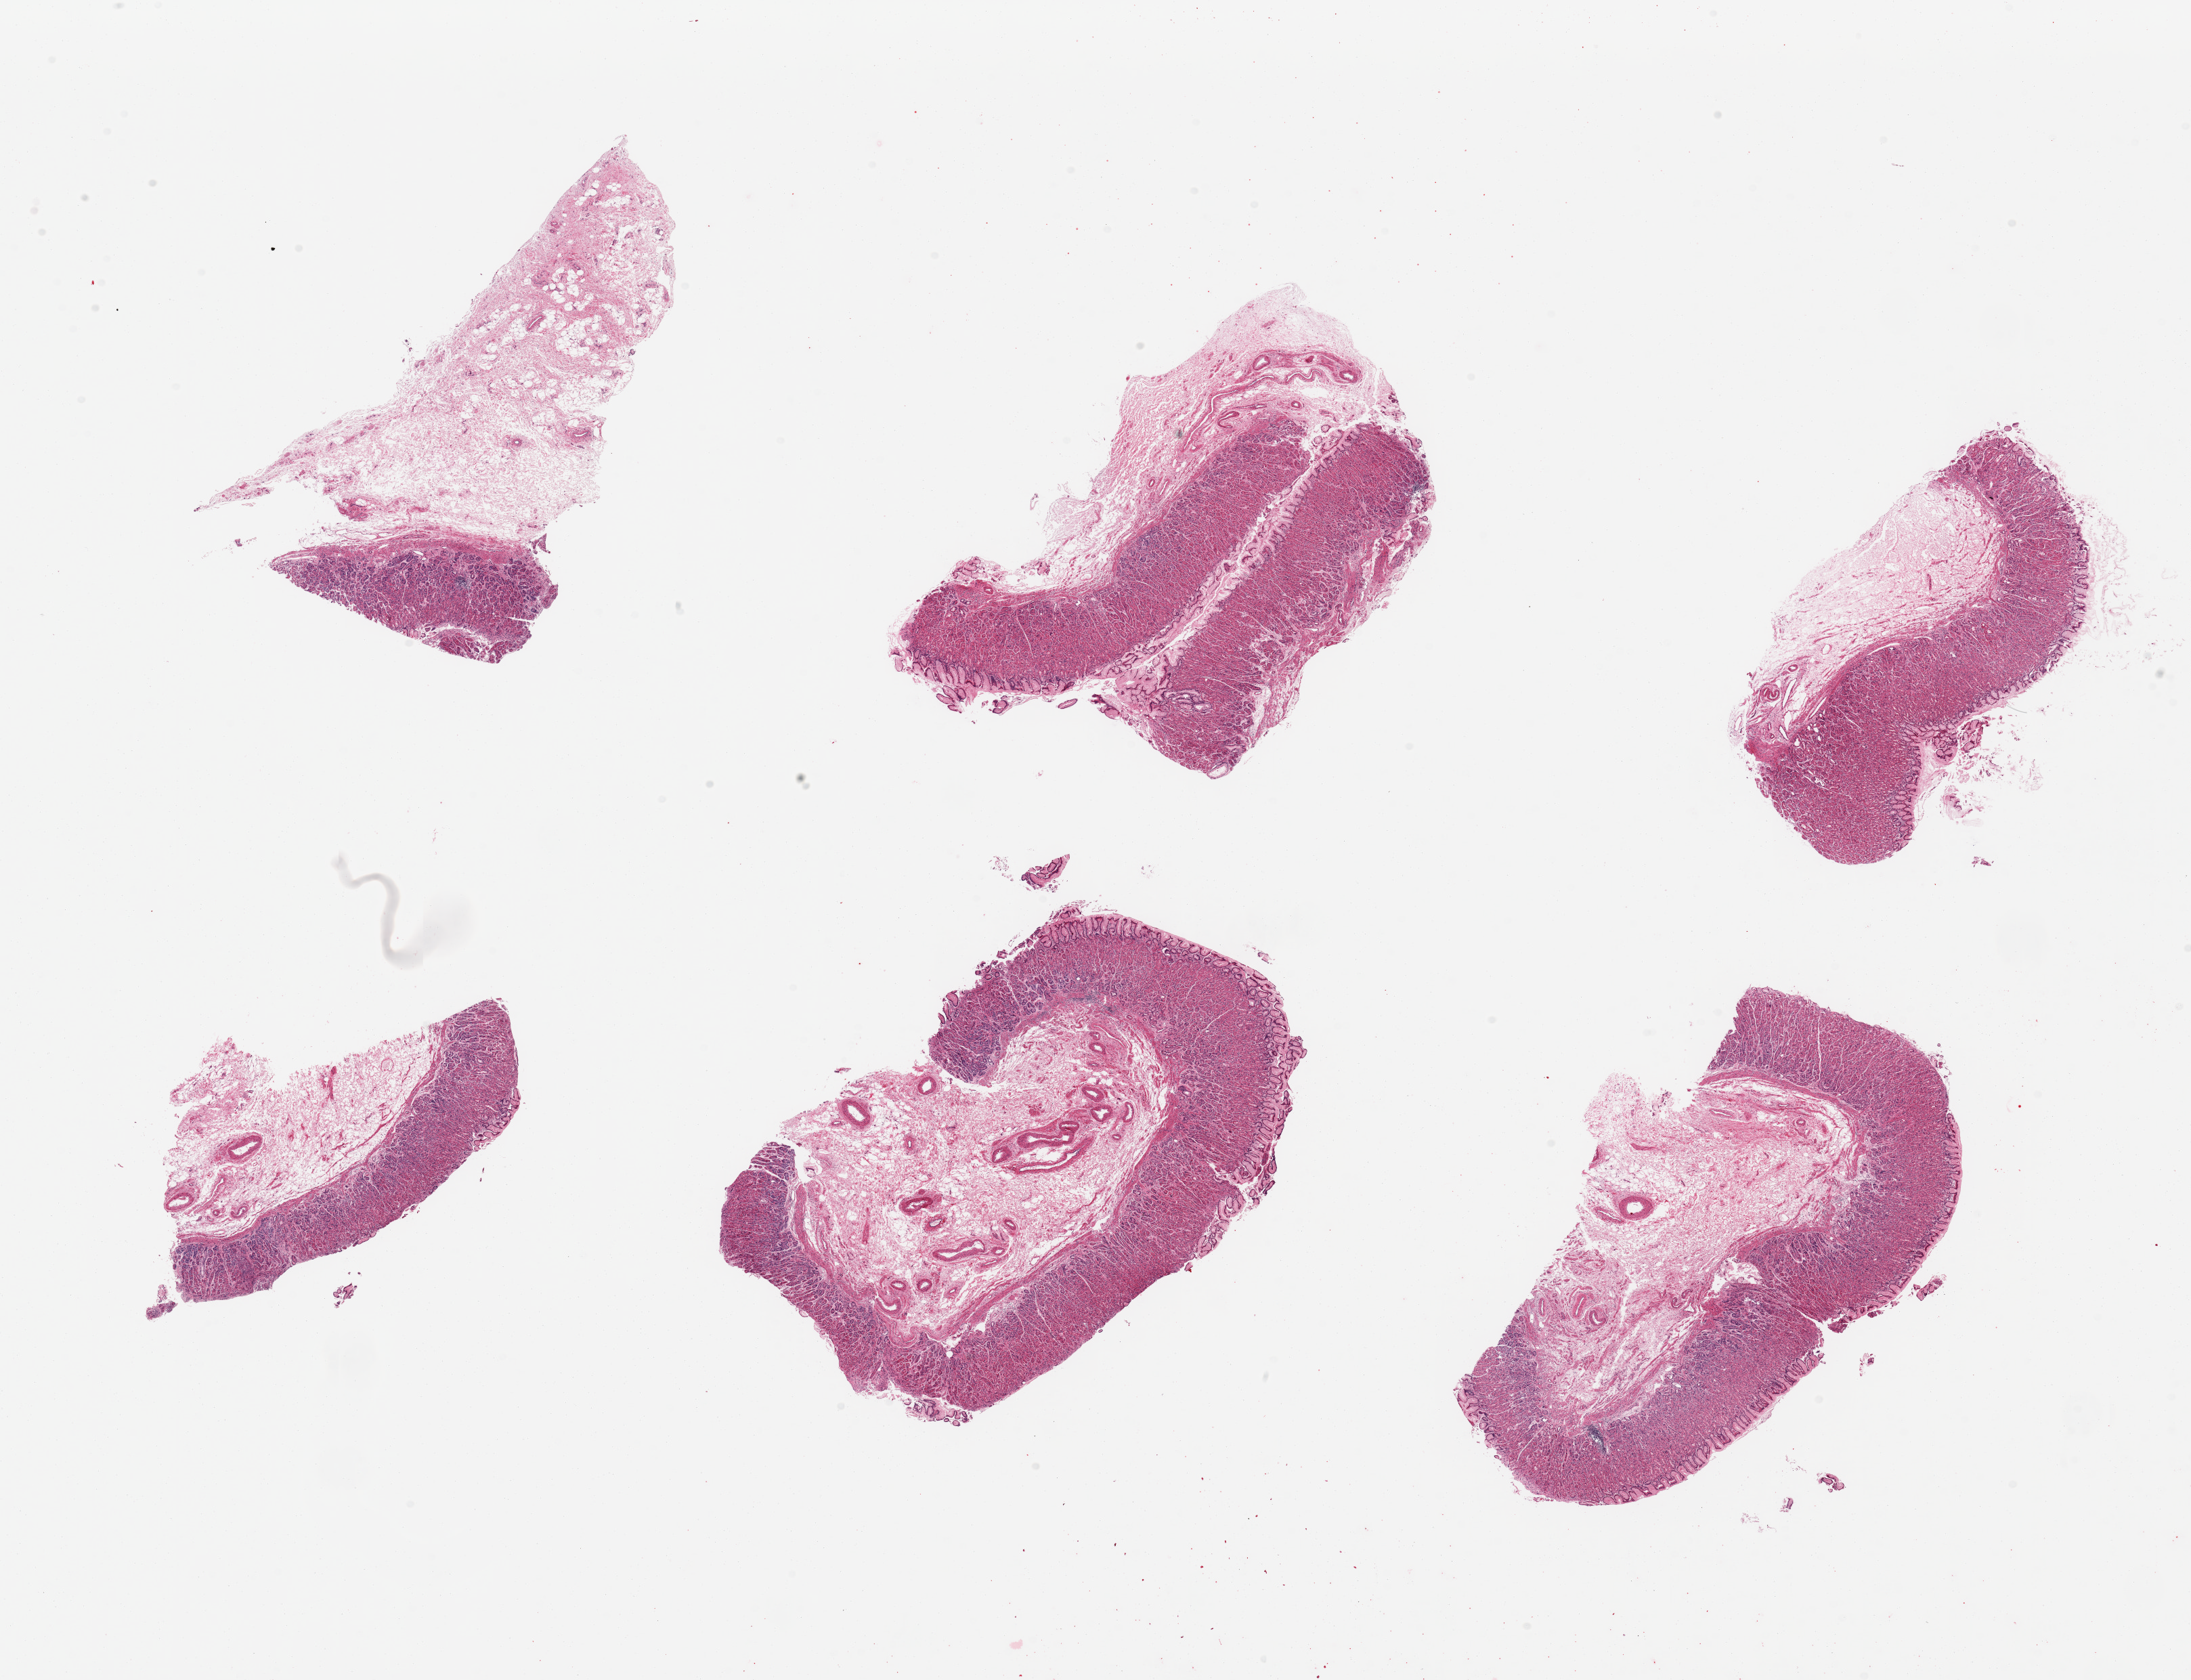
Whole-slide image, H&E stain, brightfield — whole scanned area (about 25.6 x 19.6 mm, from a 20x scan) shown as a low-resolution overview; PAXgene-fixed paraffin-embedded (PFPE) section; target tissue: gastroesophageal junction; tissue donor sample.
Reviewer comment on this tissue sample: 6 pieces, gastric mucosa, not correct target.